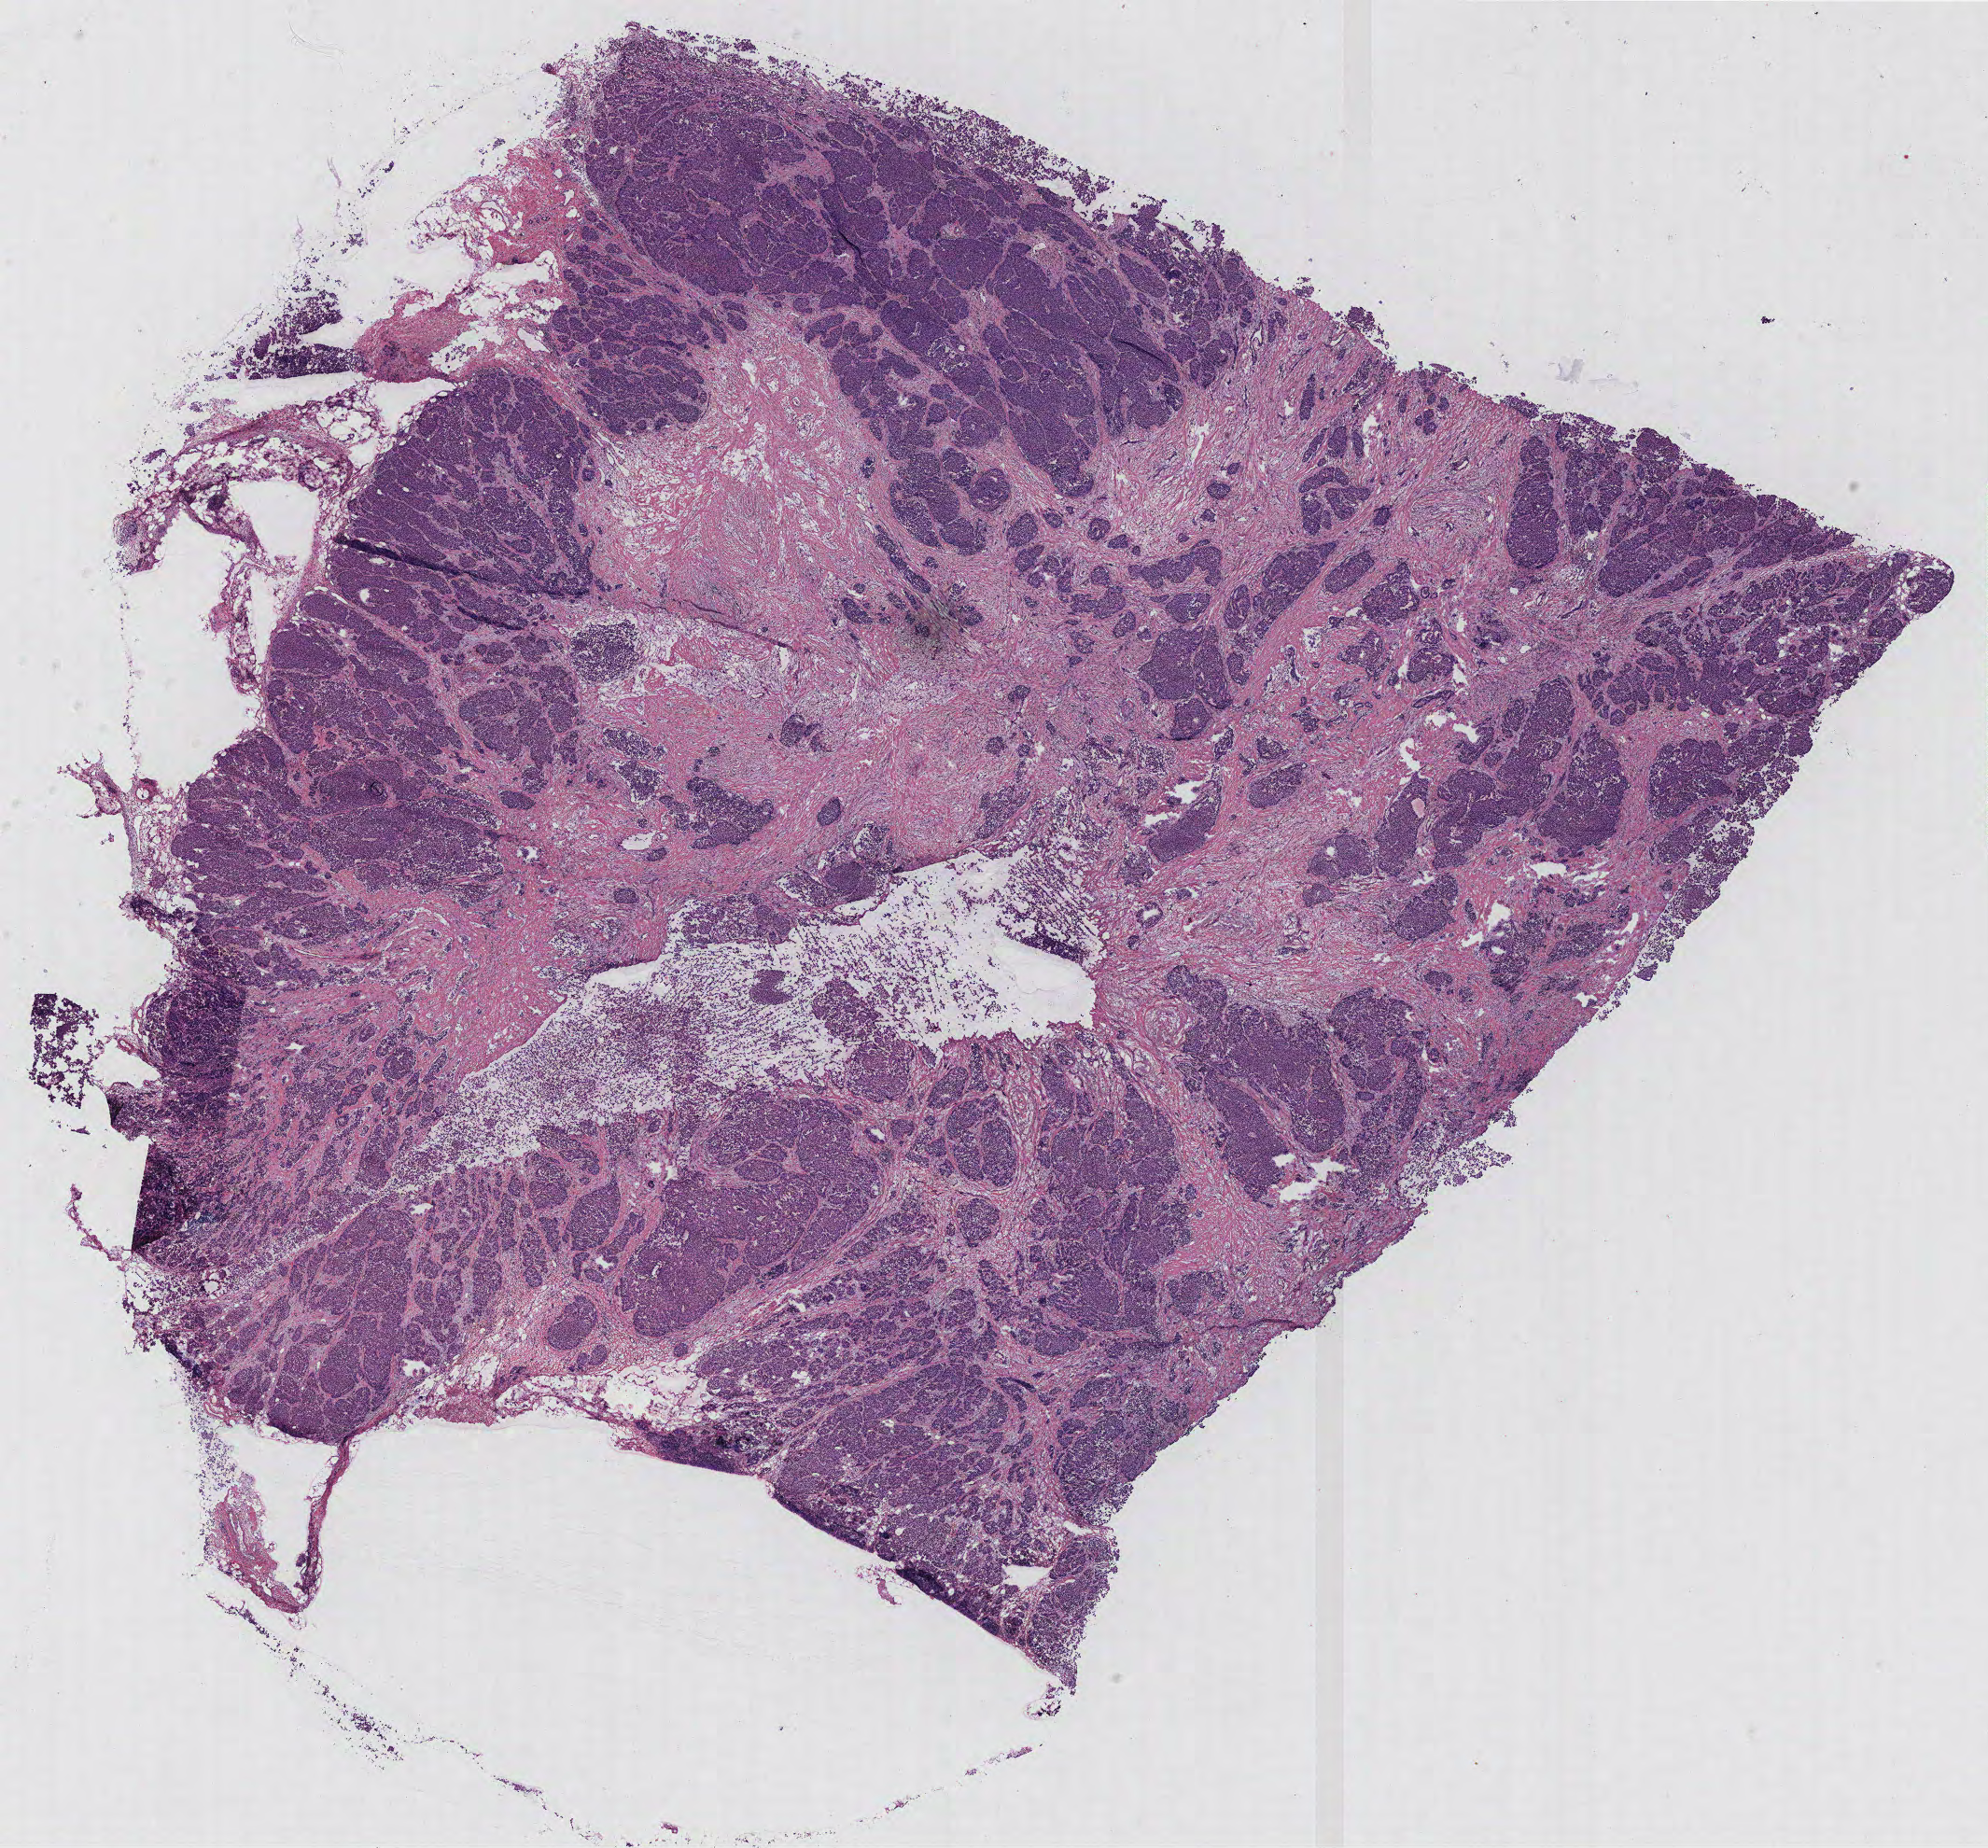
Digitized Hematoxylin and eosin (H&E) stained tissue section (whole slide) — low-resolution overview of the scanned area, about 17.0 x 15.8 mm; breast, tissue type not recorded. Female, 84 y/o.
- patient diagnosis: Infiltrating duct carcinoma, NOS